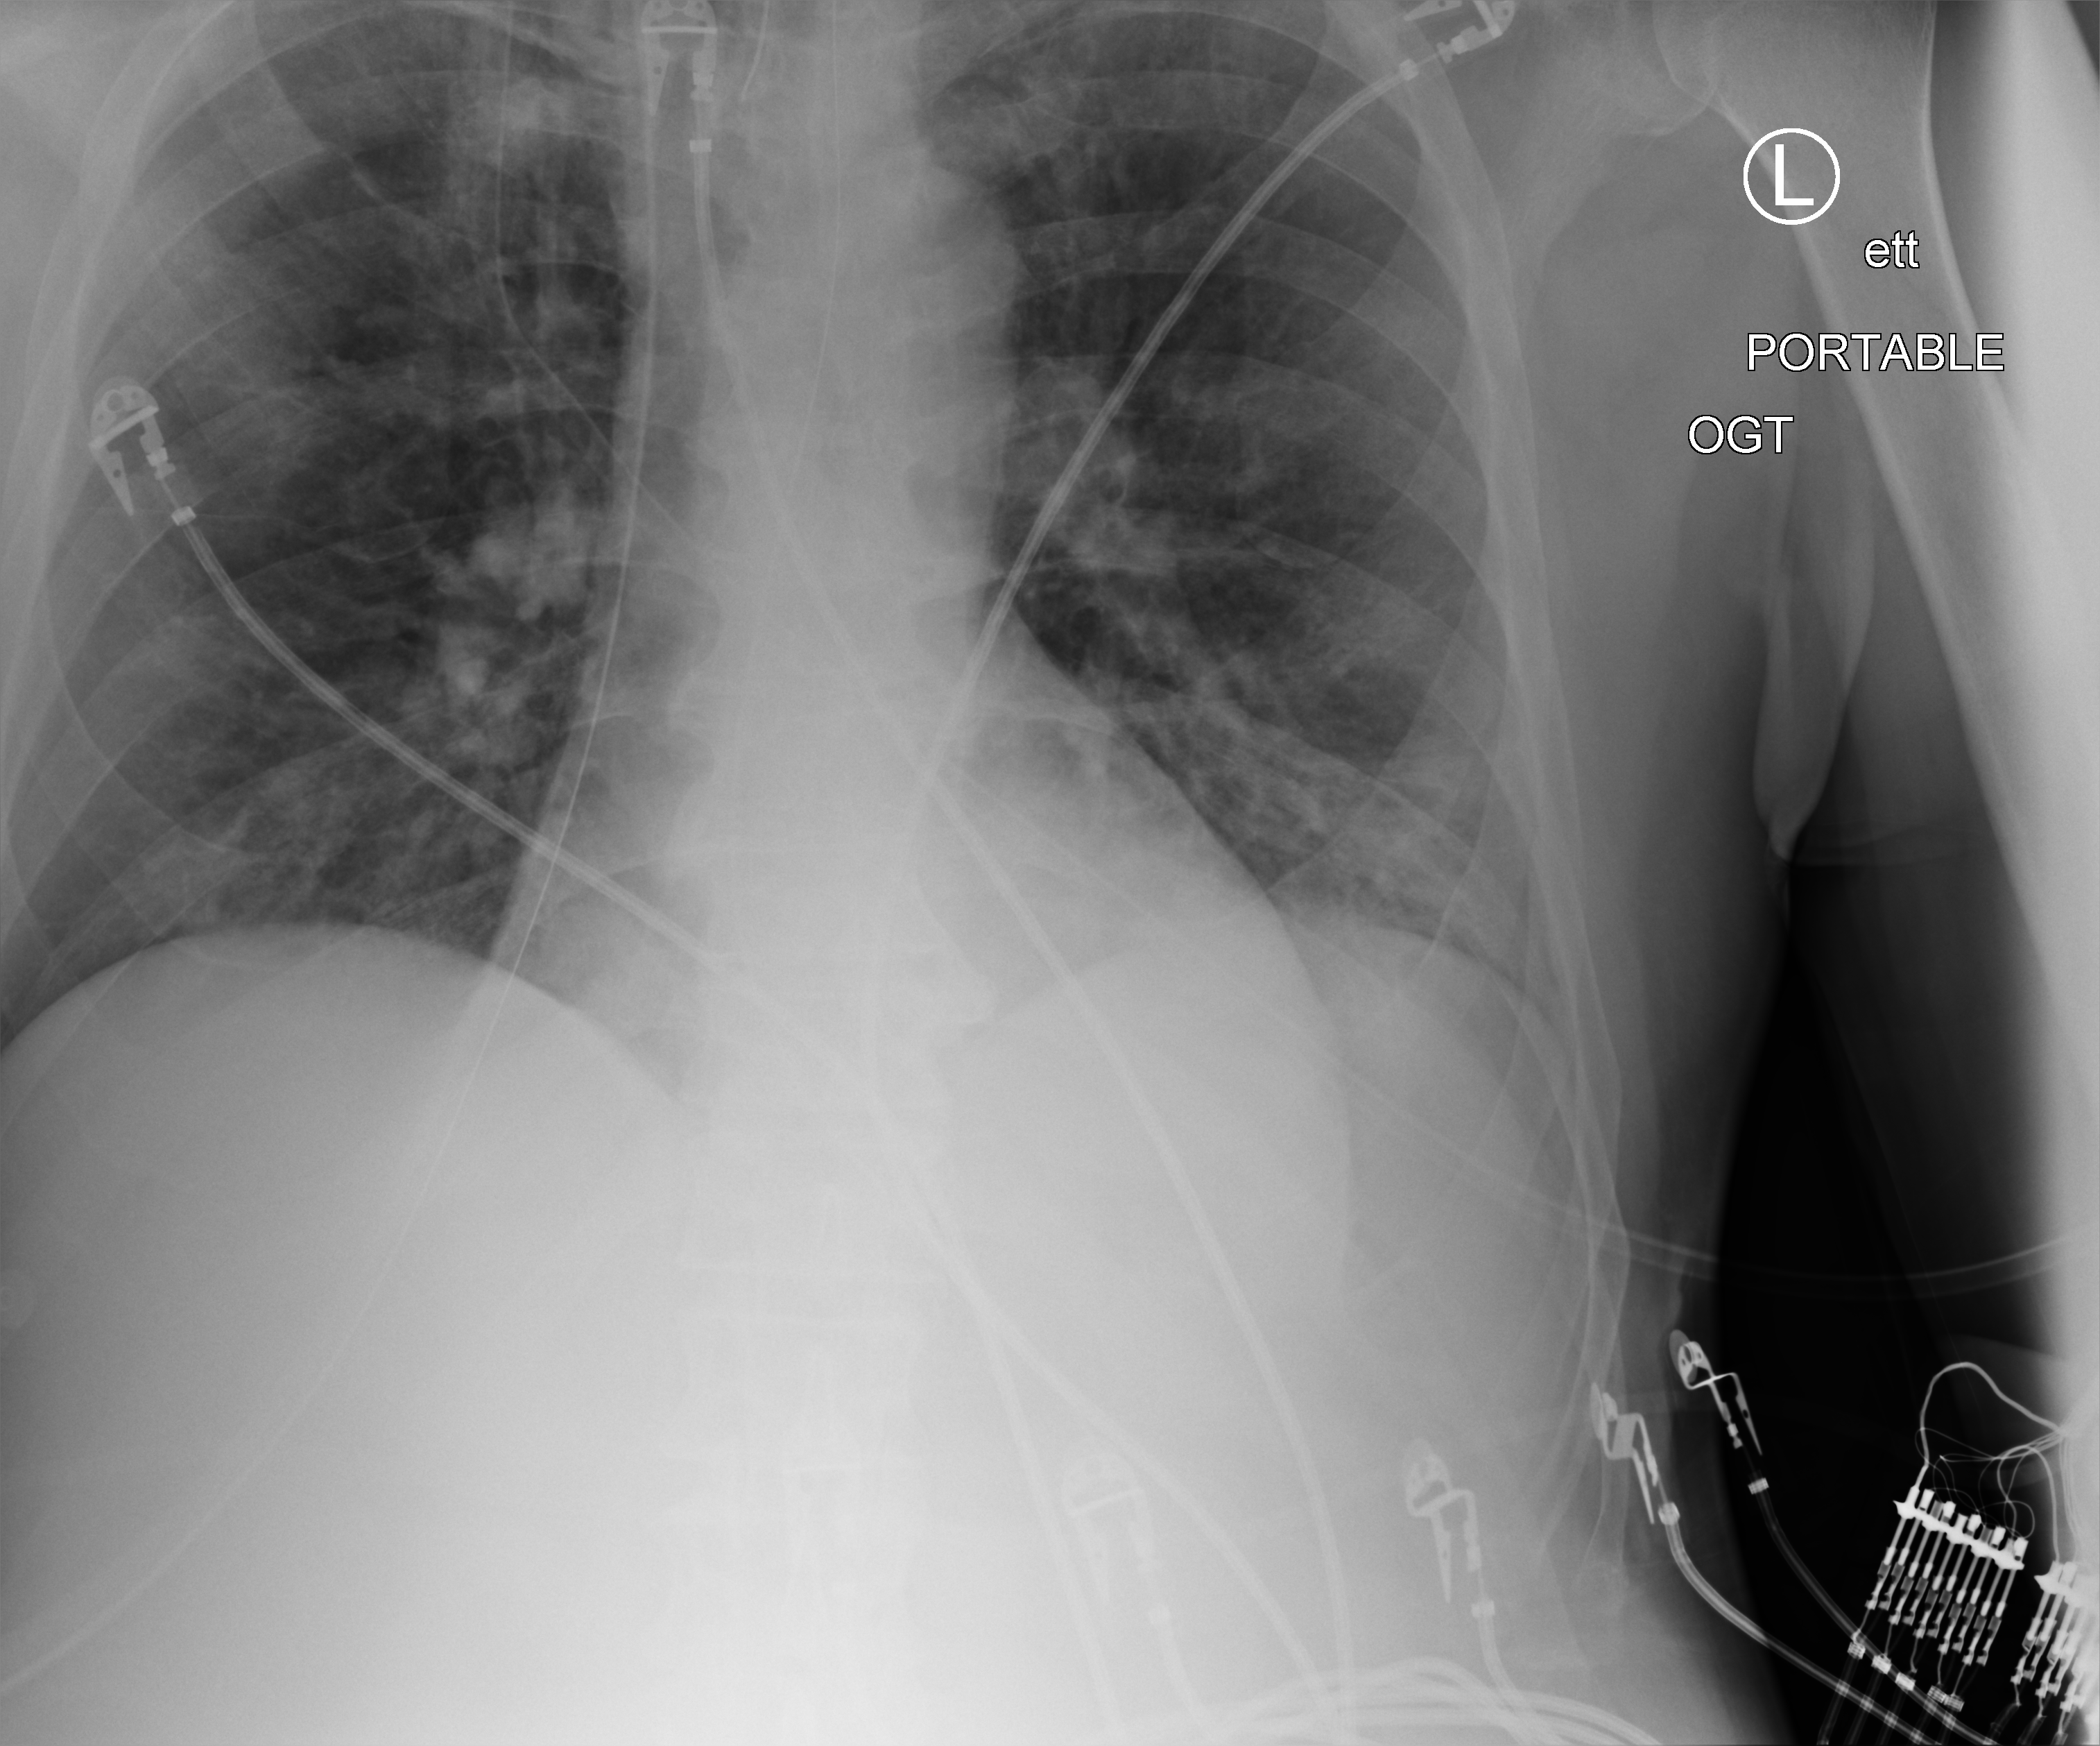
Portable chest radiograph. Patient hospitalised with COVID-19; male, aged 60–74 years.
Admission-level facts for this patient (not findings on this image; timing relative to this image not recorded): admitted to intensive care during this hospital stay: yes.